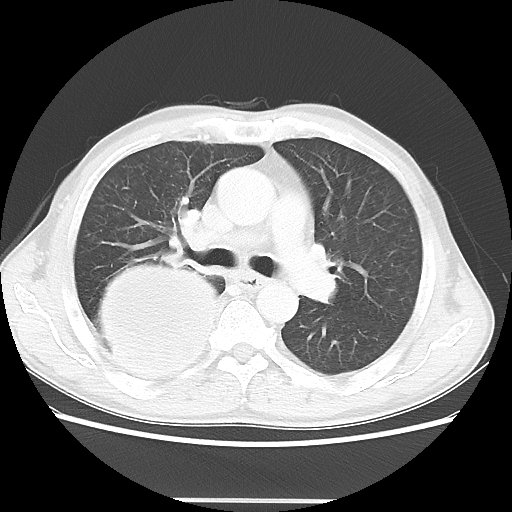
Chest CT, one axial slice; slice 30 of 48 in the series (ordered by position); 100 kVp; lung window (W 1500 / L -600 HU); 5 mm slice thickness; 512 × 512 image matrix, field of view 361 × 361 mm. Patient: male, 66 years. From the clinical record (not read from this slice): clinical TNM (as recorded): T4 N1 M1.
Annotated regions visible in this slice (bounding box drawn by a radiologist):
- lung tumour (recorded histology: small cell carcinoma): bounding box (x1, y1, x2, y2) in pixels: (87, 254, 226, 386)